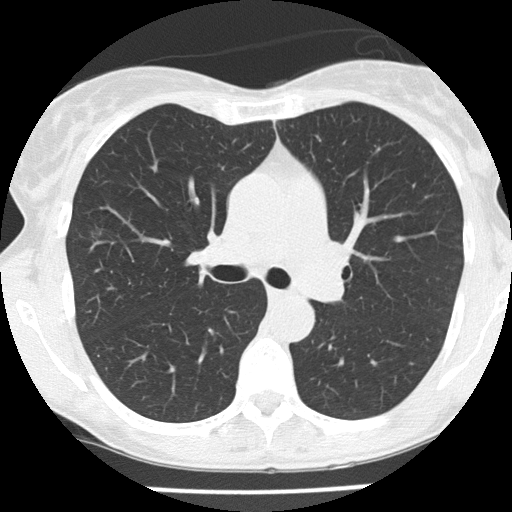
Axial slice from a low-dose chest CT screening exam, first (baseline) screen, lung window (W 1500 / L -600 HU), 2 mm slice thickness, 120 kVp, slice 61 of 166 in the series. Female participant, aged 56 years at enrolment. Former smoker at enrolment.
Lesion marked by an expert reader, box from (x=79, y=219) to (x=115, y=248) px. The exam's reader record, not a measurement of the box and not confirmed to be the same lesion: non-calcified nodule or mass ≥4 mm, right upper lobe, 7 × 5 mm, poorly defined margins, ground glass attenuation. Official screen result: positive, change unspecified: nodule(s) >= 4 mm or enlarging nodule(s), mass(es), or other non-specific abnormalities suspicious for lung cancer. Later outcome: lung cancer diagnosed 148 days after this screen — bronchiolo-alveolar carcinoma, non-mucinous, right upper lobe, well differentiated (G1), stage IA (AJCC 6th edition), 6 mm at pathology.